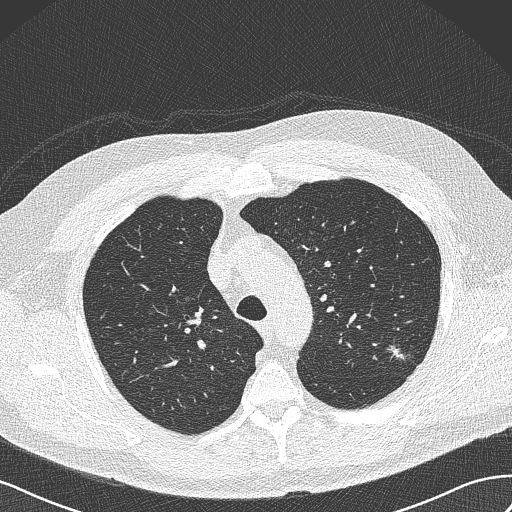
Chest CT (low-dose screening protocol), one axial image. Baseline screening round. Lung window (W 1500 / L -600 HU). Lung (sharp) reconstruction kernel (B50f). Male participant, aged 65 years at enrolment. Former smoker at enrolment.
- Expert-annotated lung lesion, box from (x=383, y=341) to (x=418, y=372) px.
- The screening reader recorded 3 non-calcified nodules or masses ≥4 mm on this exam (left upper lobe, left upper lobe, right upper lobe); which of them this box marks is not recorded.
- Participant outcome: lung cancer diagnosed 541 days after this screen (after the second annual screen) — adenocarcinoma, NOS, left upper lobe, poorly differentiated (G3), stage IA (AJCC 6th edition), 13 mm at pathology.